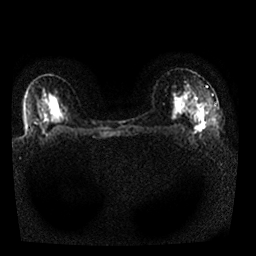
Breast MRI, one axial slice; slice 17 of 25 in the series (ordered by position); diffusion-weighted series; image 2 of 4 stored at this slice position (different b-values; order by instance number); 1.5 T; 4 mm slice thickness; 256 × 256 image matrix, field of view 330 × 330 mm. Female patient.
Structures marked on this image (manually delineated by an expert):
- tumour on diffusion-weighted imaging: box from (x=197, y=124) to (x=205, y=130) px